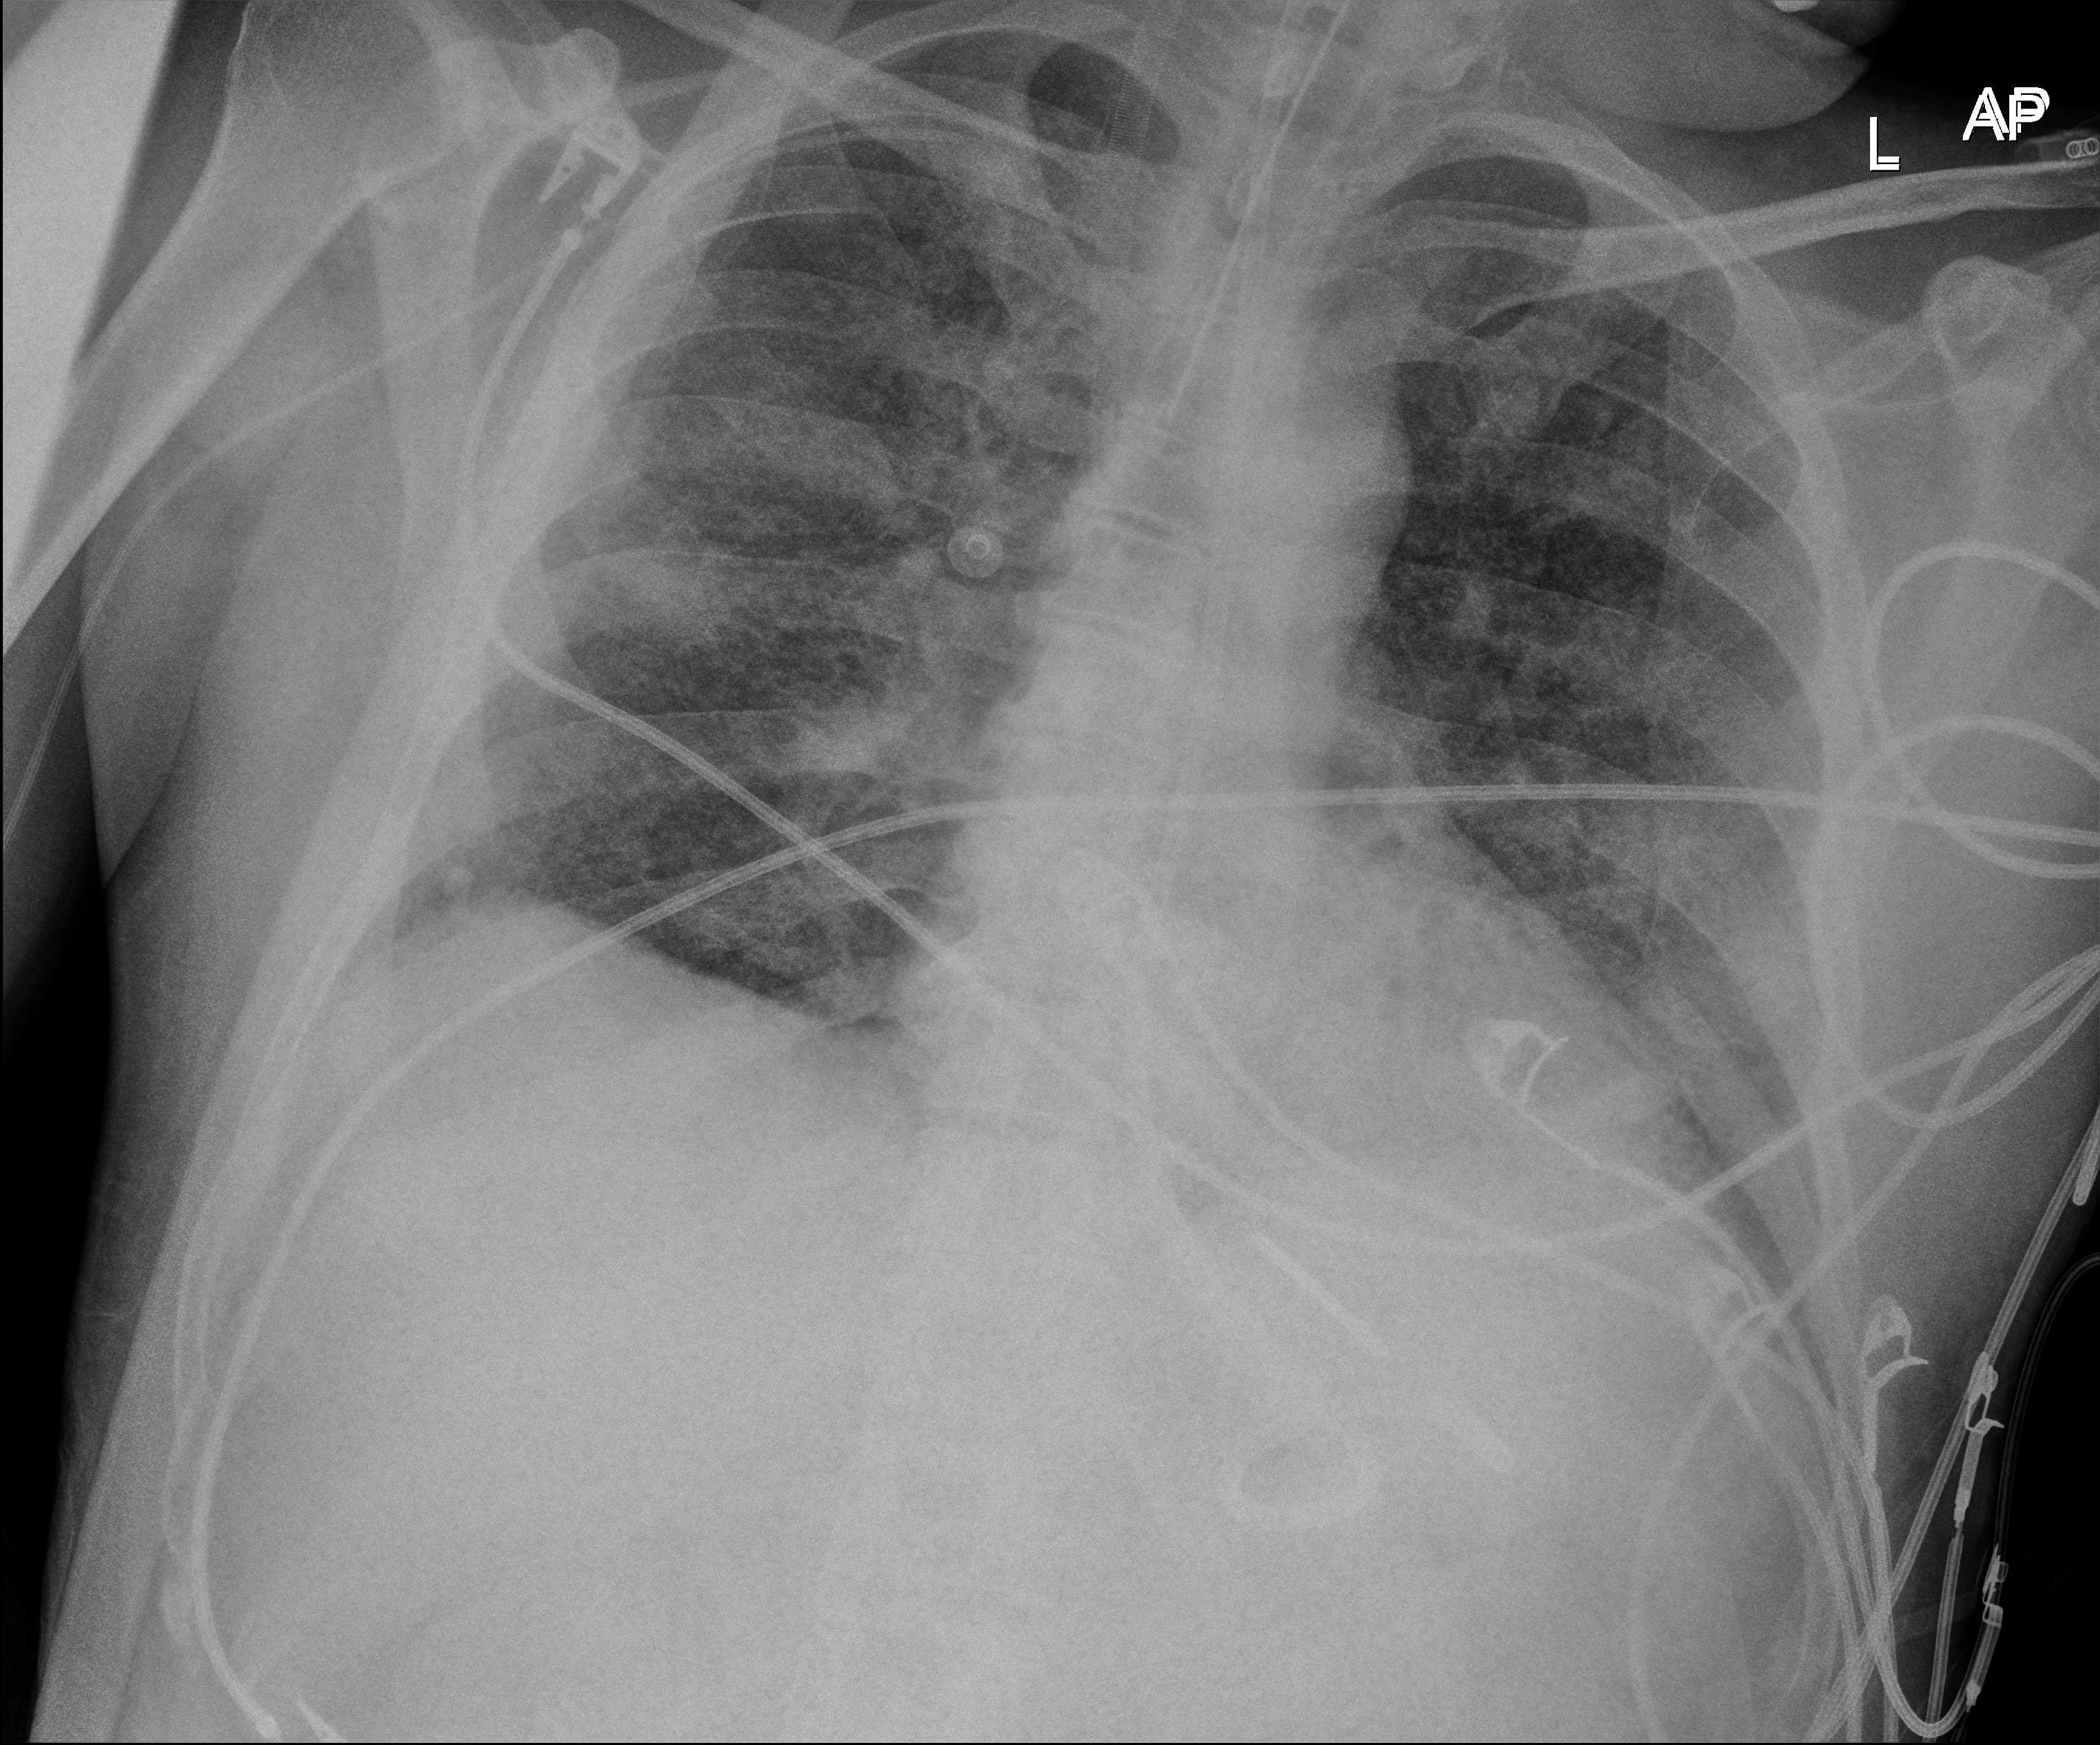
Chest X-ray (portable), anteroposterior (AP) projection. Patient hospitalised with COVID-19; male, aged 18–59 years.
Admission-level facts for this patient (not findings on this image; timing relative to this image not recorded): mechanically ventilated during this hospital stay: yes.